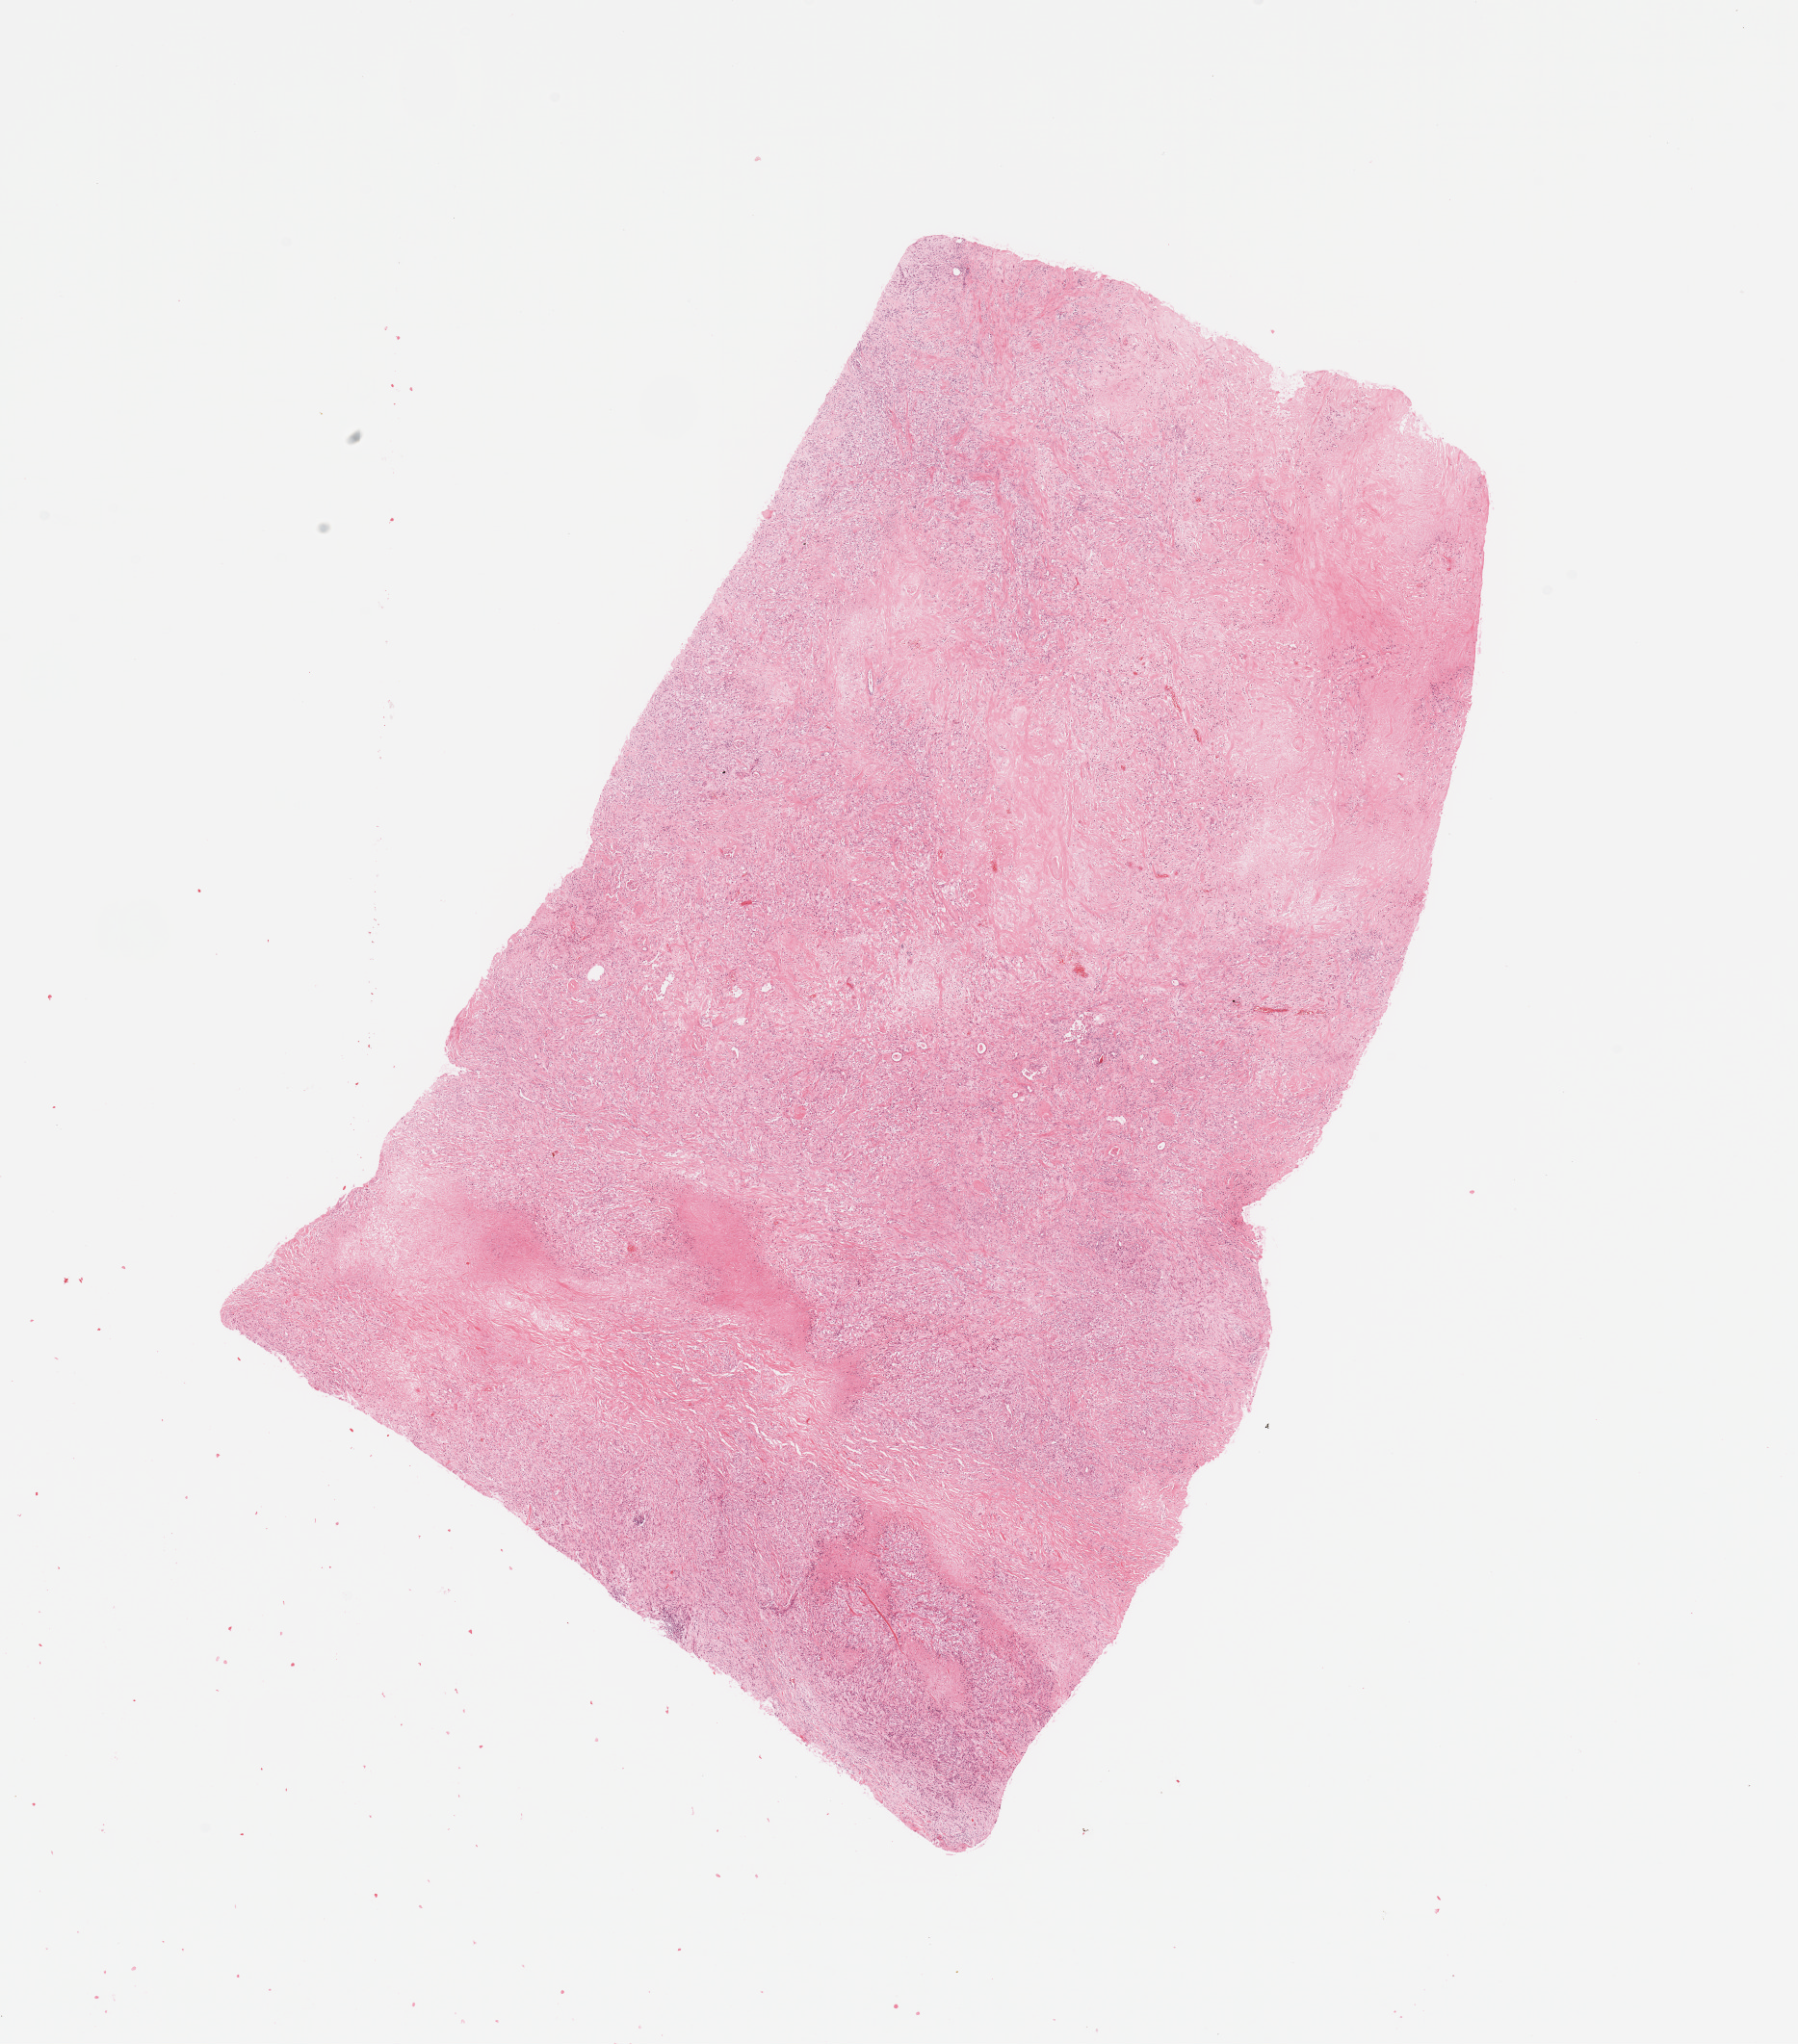
Digitized H&E tissue section (whole slide), whole scanned area (about 14.8 x 16.8 mm, acquisition: 20x scan) shown as a low-resolution overview, tumour tissue sample, sampled site: kidney. Patient: female, age 68 years. Histologic grade: G3 (poorly differentiated). Slide review estimates, as recorded: tumour nuclei 80%, necrosis 10%.
* diagnosis: Renal cell carcinoma, NOS
* AJCC pathologic stage: IV